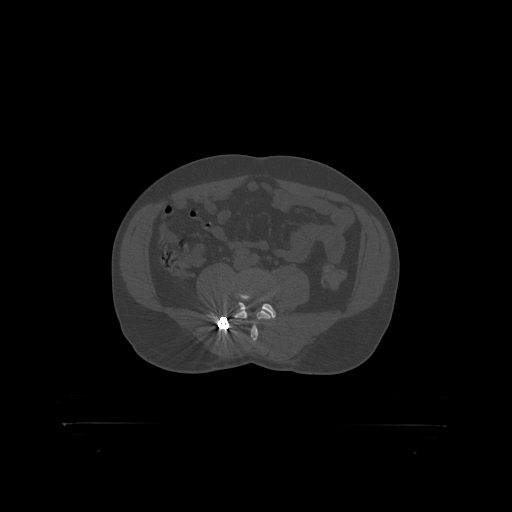
CT including the spine, one axial slice; position 221 of 399 along the scan axis; reconstruction kernel STANDARD; 120 kVp; bone window (W 1800 / L 400 HU); 1.25 mm slice thickness; 512 × 512 image matrix. Male patient, age 46 years. Case-level facts recorded for this patient, not image findings: primary cancer: skin.
Annotated regions visible in this slice (semi-automatically segmented with operator editing):
- L4 vertebra: bounding box [x1, y1, x2, y2] px = [235, 310, 272, 319]
- L5 vertebra: [225, 294, 277, 317]